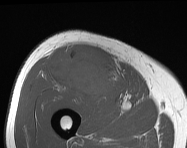
MRI of an extremity soft-tissue mass, one axial slice. Position 74 of 114 along the scan axis. MR volume resampled by the dataset authors to the PET/CT grid (not the native acquisition matrix). 3.27 mm slice thickness. 187 × 148 image matrix. Male patient. From the clinical record (not read from this slice): histological type: pleiomorphic leiomyosarcoma; grade: intermediate; site of the primary tumour: right thigh.
Outlined on this slice (expert contour drawn on MRI and transferred to this co-registered scan by the dataset authors):
- gross tumour volume including surrounding oedema: bounding box [x1, y1, x2, y2] px = [50, 47, 117, 96]
- gross tumour volume (mass): [50, 47, 117, 96]